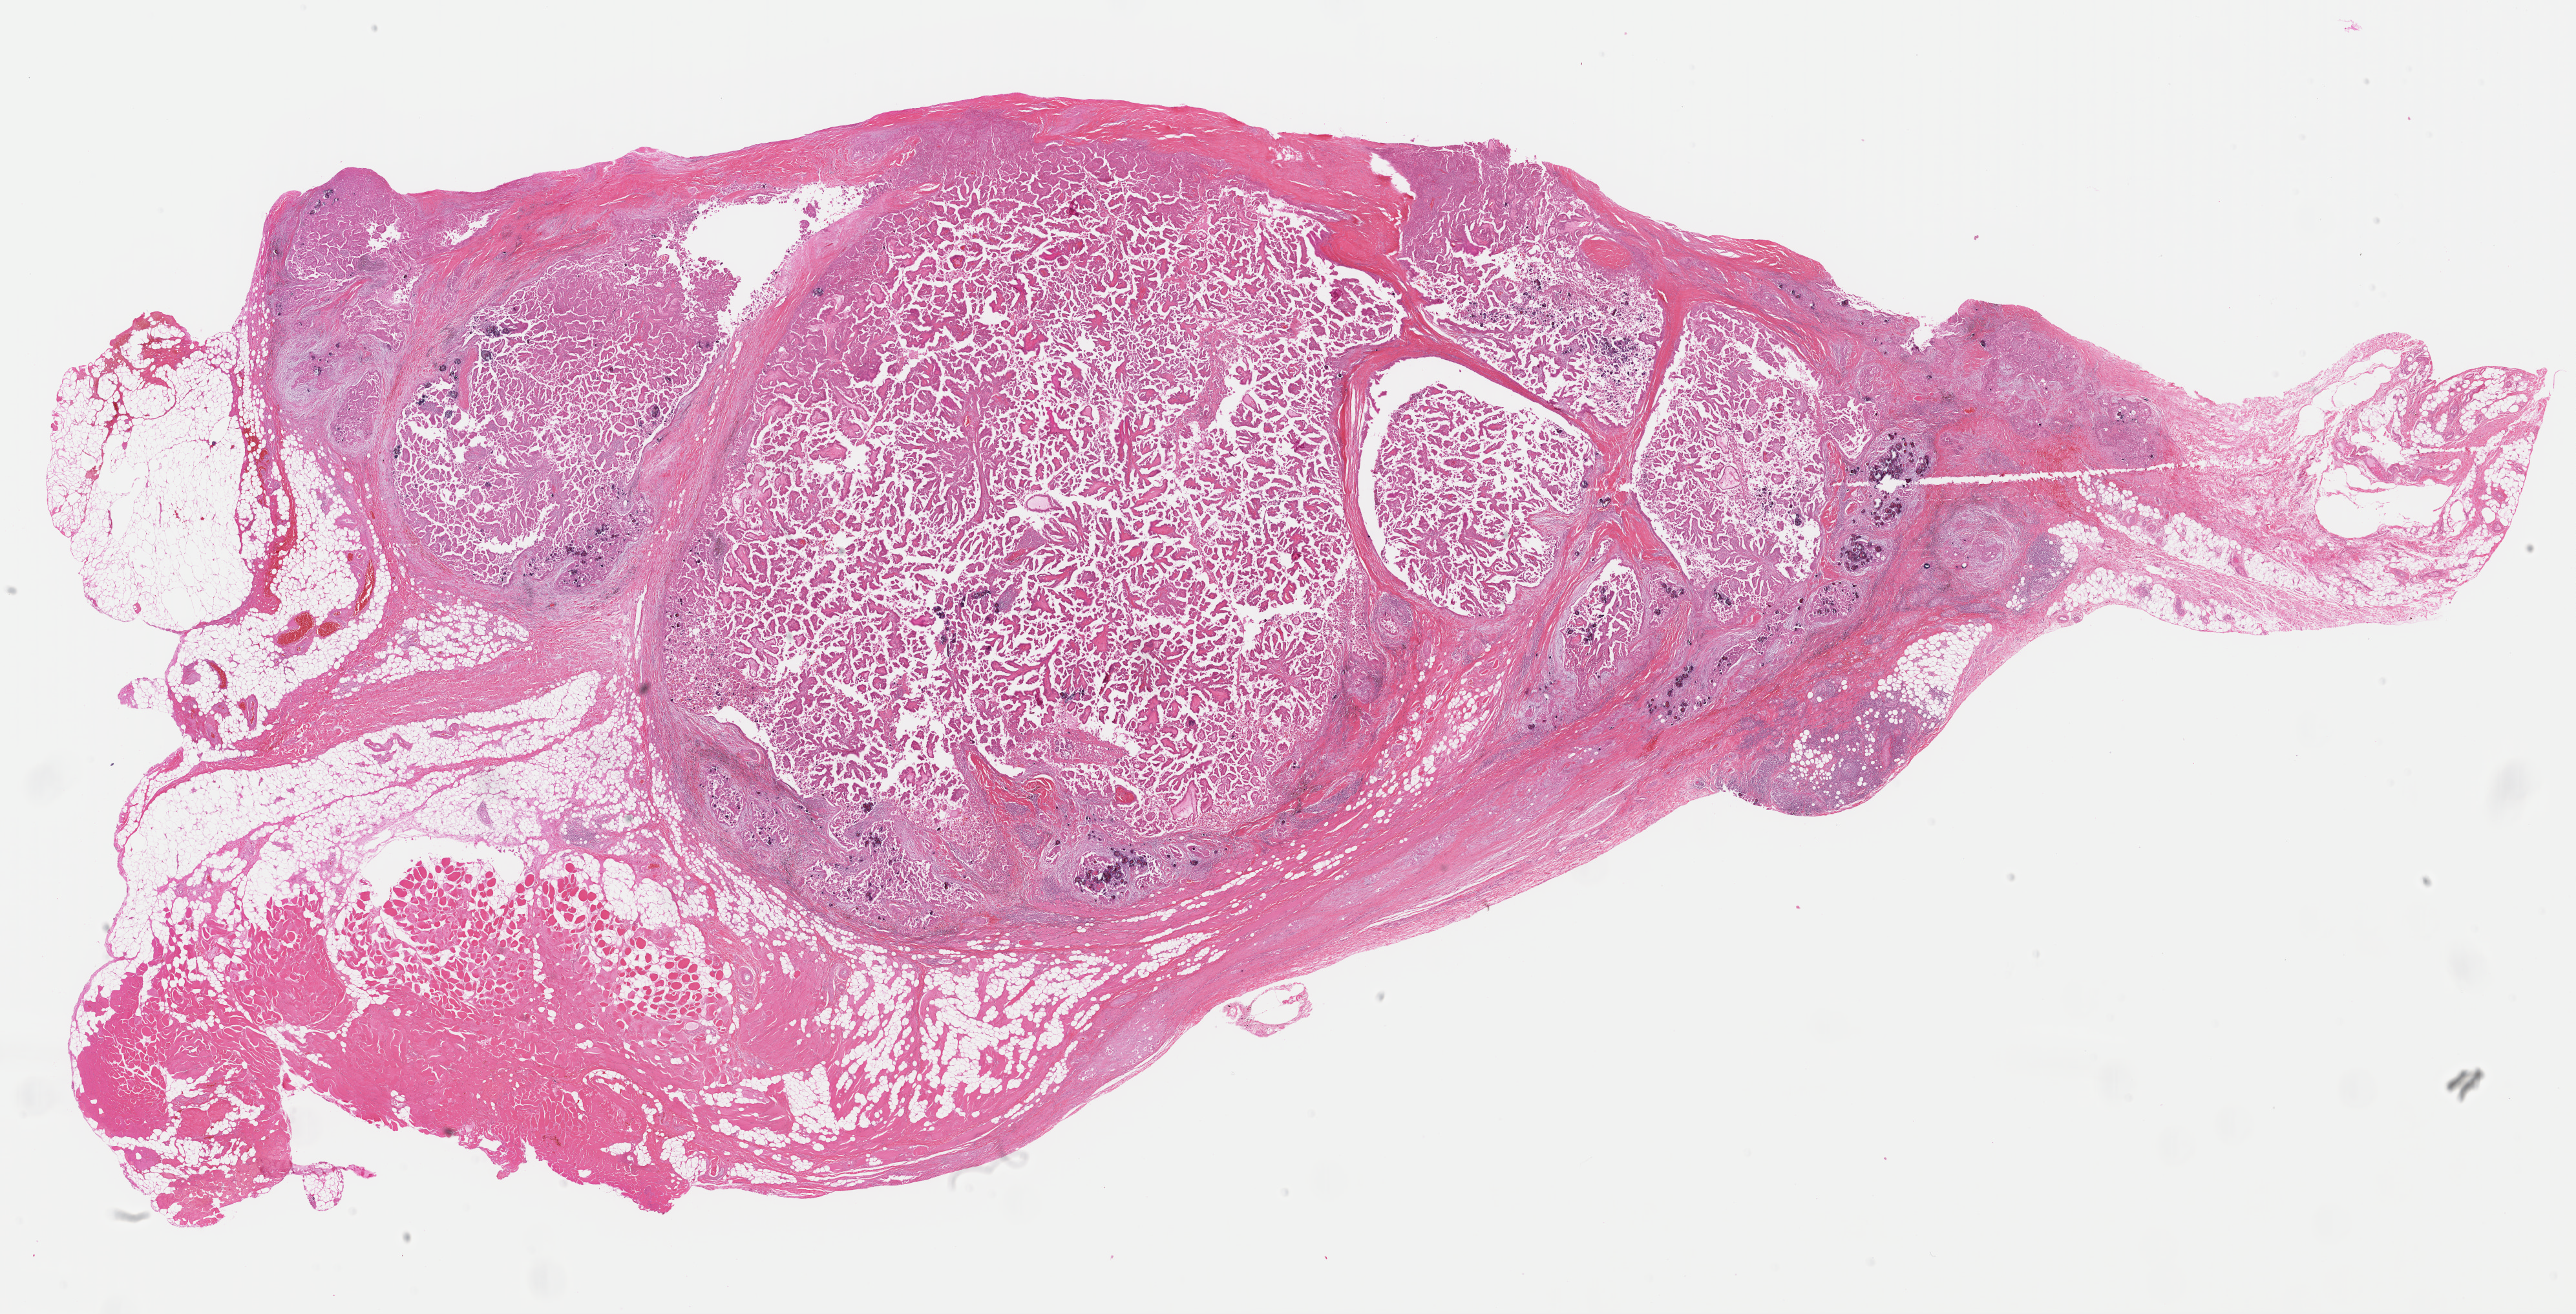
Whole-slide histology image, H&E-stained, whole scanned area (about 31.5 x 16.1 mm) shown as a low-resolution overview; formalin-fixed paraffin-embedded (FFPE) diagnostic section; thyroid, primary tumour sample. Patient: male, age at initial diagnosis 60 years.
AJCC pathologic stage: IVA (6th edition). Laterality: right. TNM: T4a N1 M0. Pathologic diagnosis: Papillary adenocarcinoma, NOS (thyroid gland). Lymph nodes positive (case pathology): 7 of 27 examined.